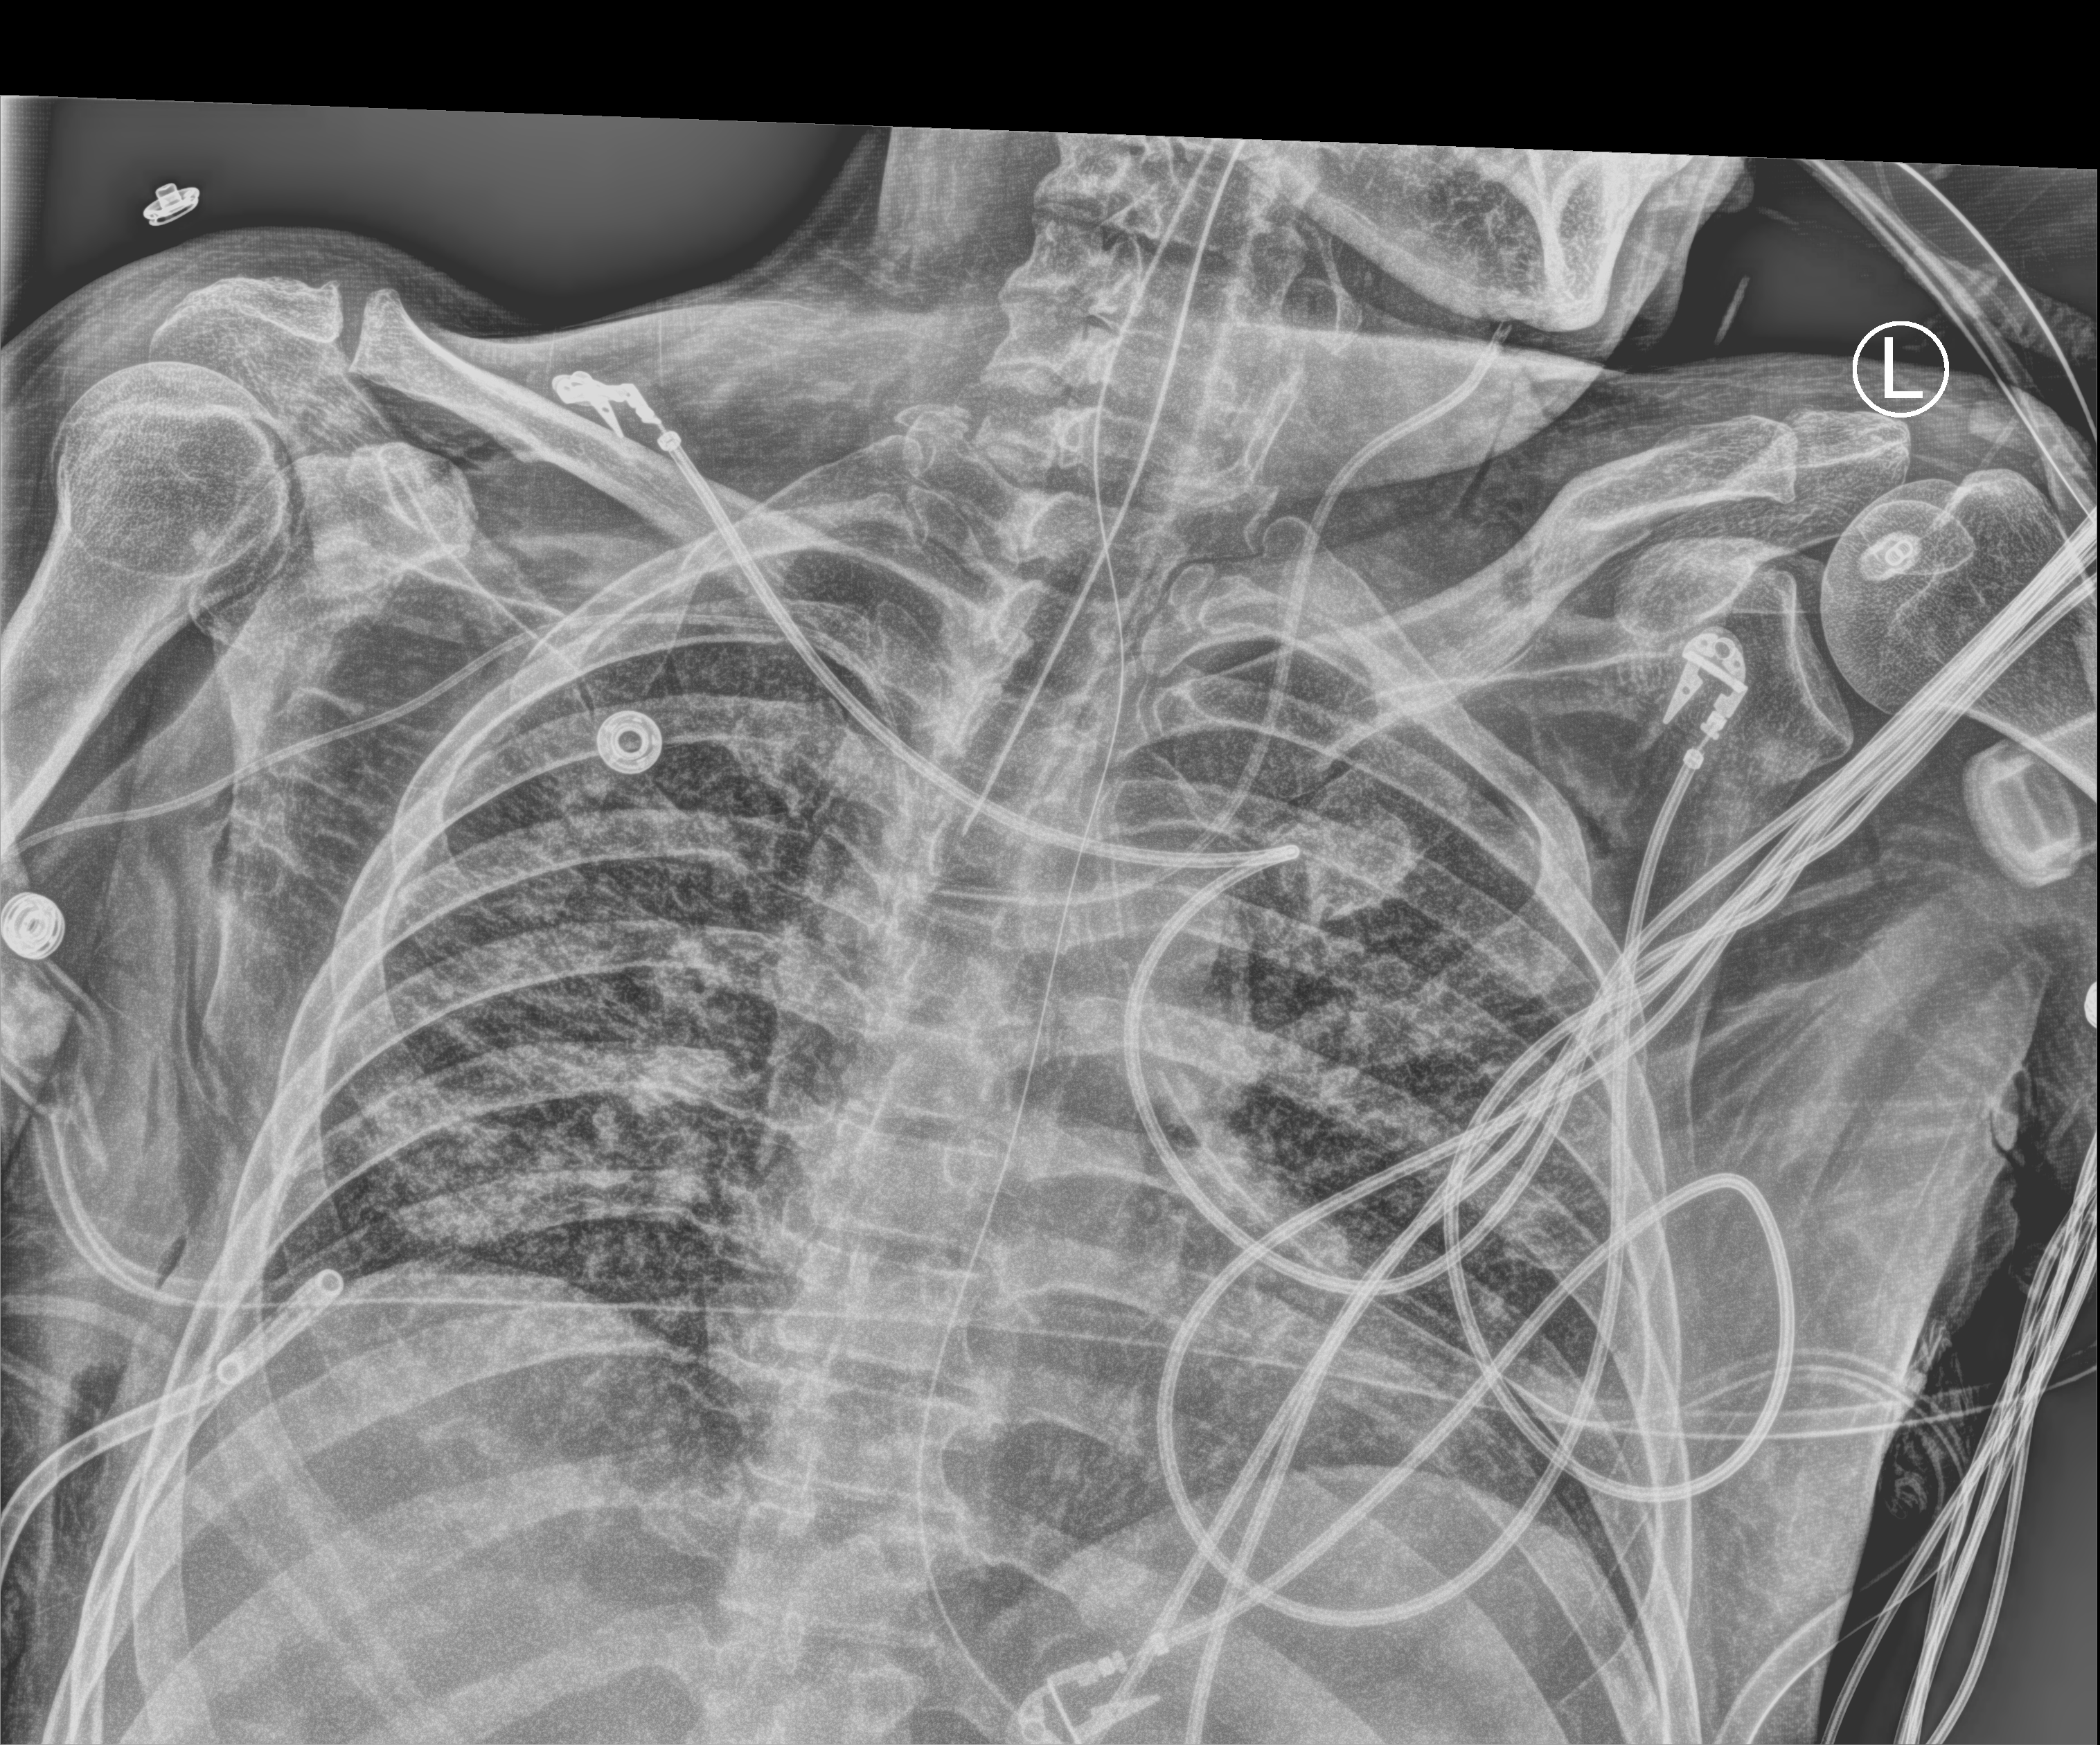
Bedside chest radiograph (computed radiography). Male patient hospitalised with COVID-19, age 18–59 years.
From the hospital-stay record, not from the radiograph (when in the stay this image was taken is not recorded): other chronic lung disease (admission record): no; length of hospital stay: 77 days; mechanically ventilated during this hospital stay: yes.